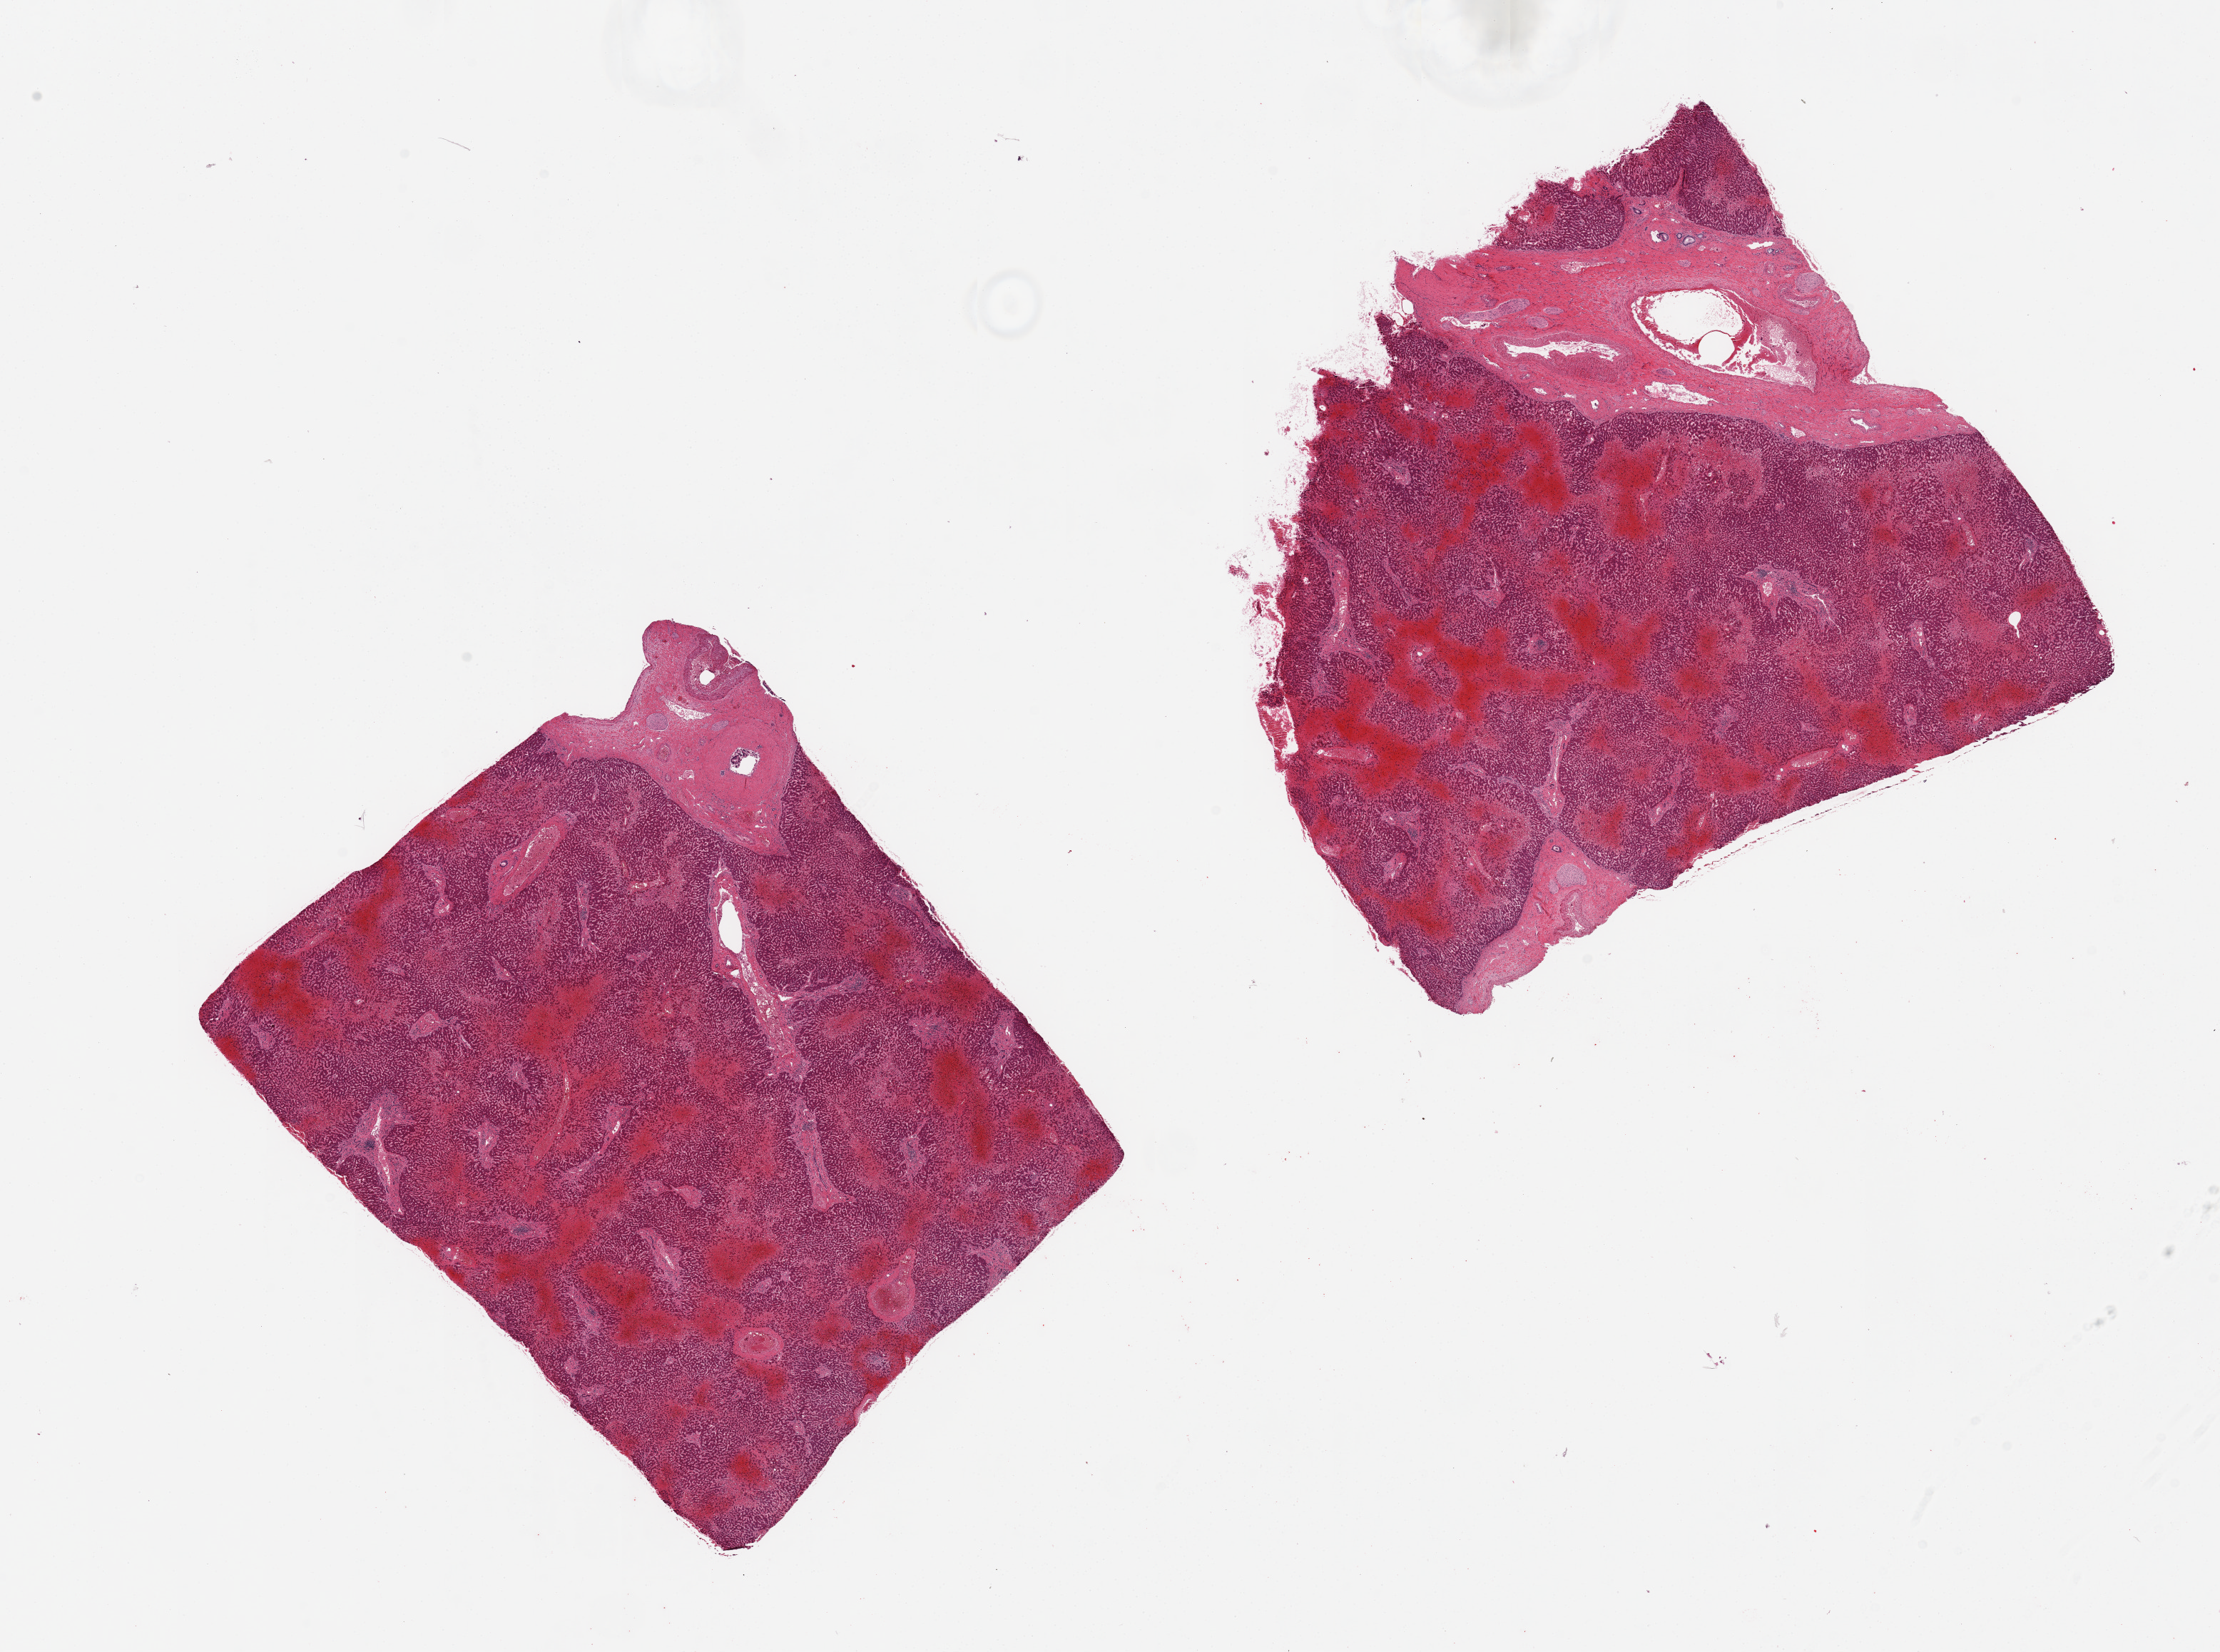
Hematoxylin and eosin (H&E) whole-slide image — low-resolution overview of the scanned area, about 24.6 x 18.3 mm. PAXgene-fixed, paraffin-embedded tissue. Section of liver (target tissue). Tissue donor sample.
Reviewer comment on this tissue sample: 2 pieces. Extensive central passive congestion and hemorrhage. Large vessels and stroma occupy 10% and 20%.